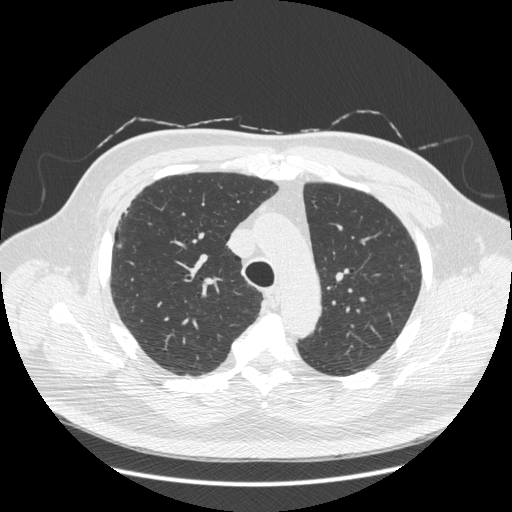
Low-dose screening chest CT, axial slice, second screening round (one year after baseline), lung window (W 1500 / L -600 HU), 1.25 mm slice thickness, slice 73 of 281 in the series. Male, age 66 years at enrolment. Current smoker at enrolment.
Expert reader's lesion annotation, bounding box (x1, y1, x2, y2) in pixels: (100, 212, 143, 260). The screening reader recorded 2 non-calcified nodules or masses ≥4 mm on this exam (right lower lobe, right lower lobe); which of them this box marks is not recorded. Later outcome: lung cancer diagnosed 403 days after this screen (after the third annual screen) — non-small cell carcinoma, right upper lobe, stage IV (AJCC 6th edition), 50 mm at pathology.